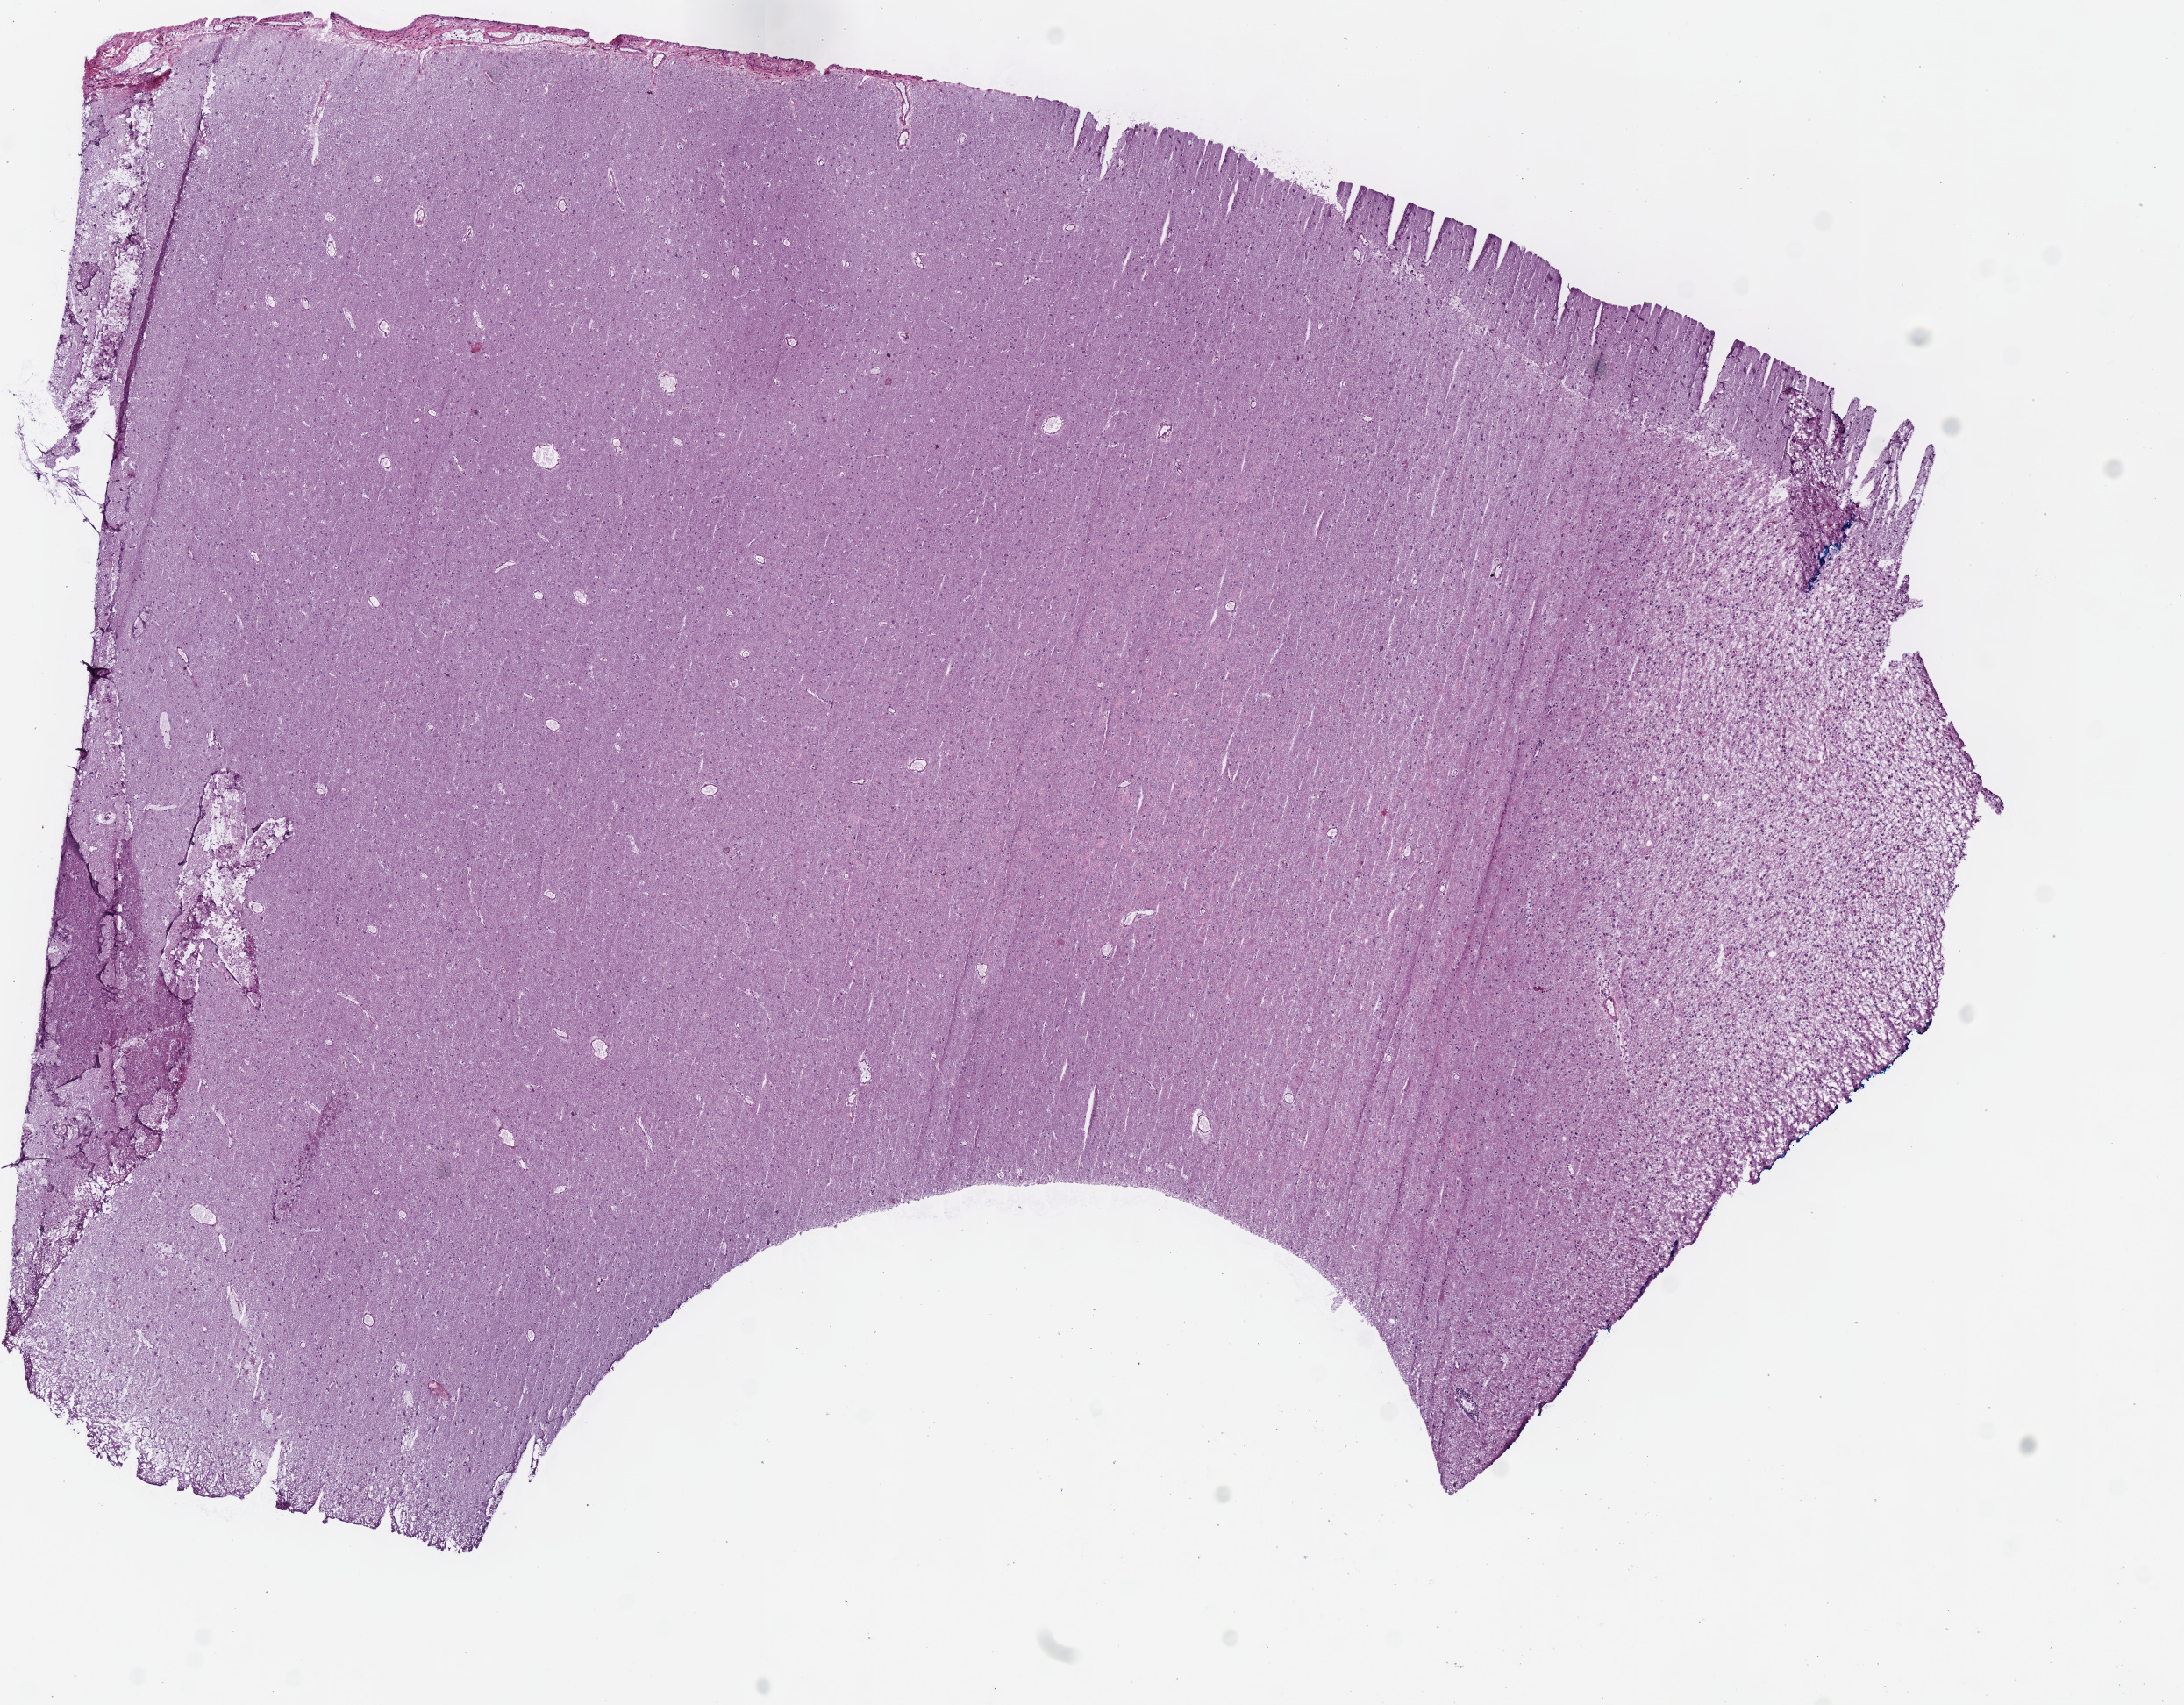
Digitized H&E tissue section (whole slide) — shown as a low-resolution overview of the whole scanned area (about 9.8 x 7.6 mm); frozen section; primary tumour sample from the brain. Male, age 23 years at initial diagnosis. Histologic grade: G3 (poorly differentiated). Slide review estimates, as recorded: tumour cells 100%, tumour nuclei 50%, normal cells 0%, stromal cells 0%, necrosis 0%.
Laterality: left. Diagnosis: Mixed glioma (cerebrum).